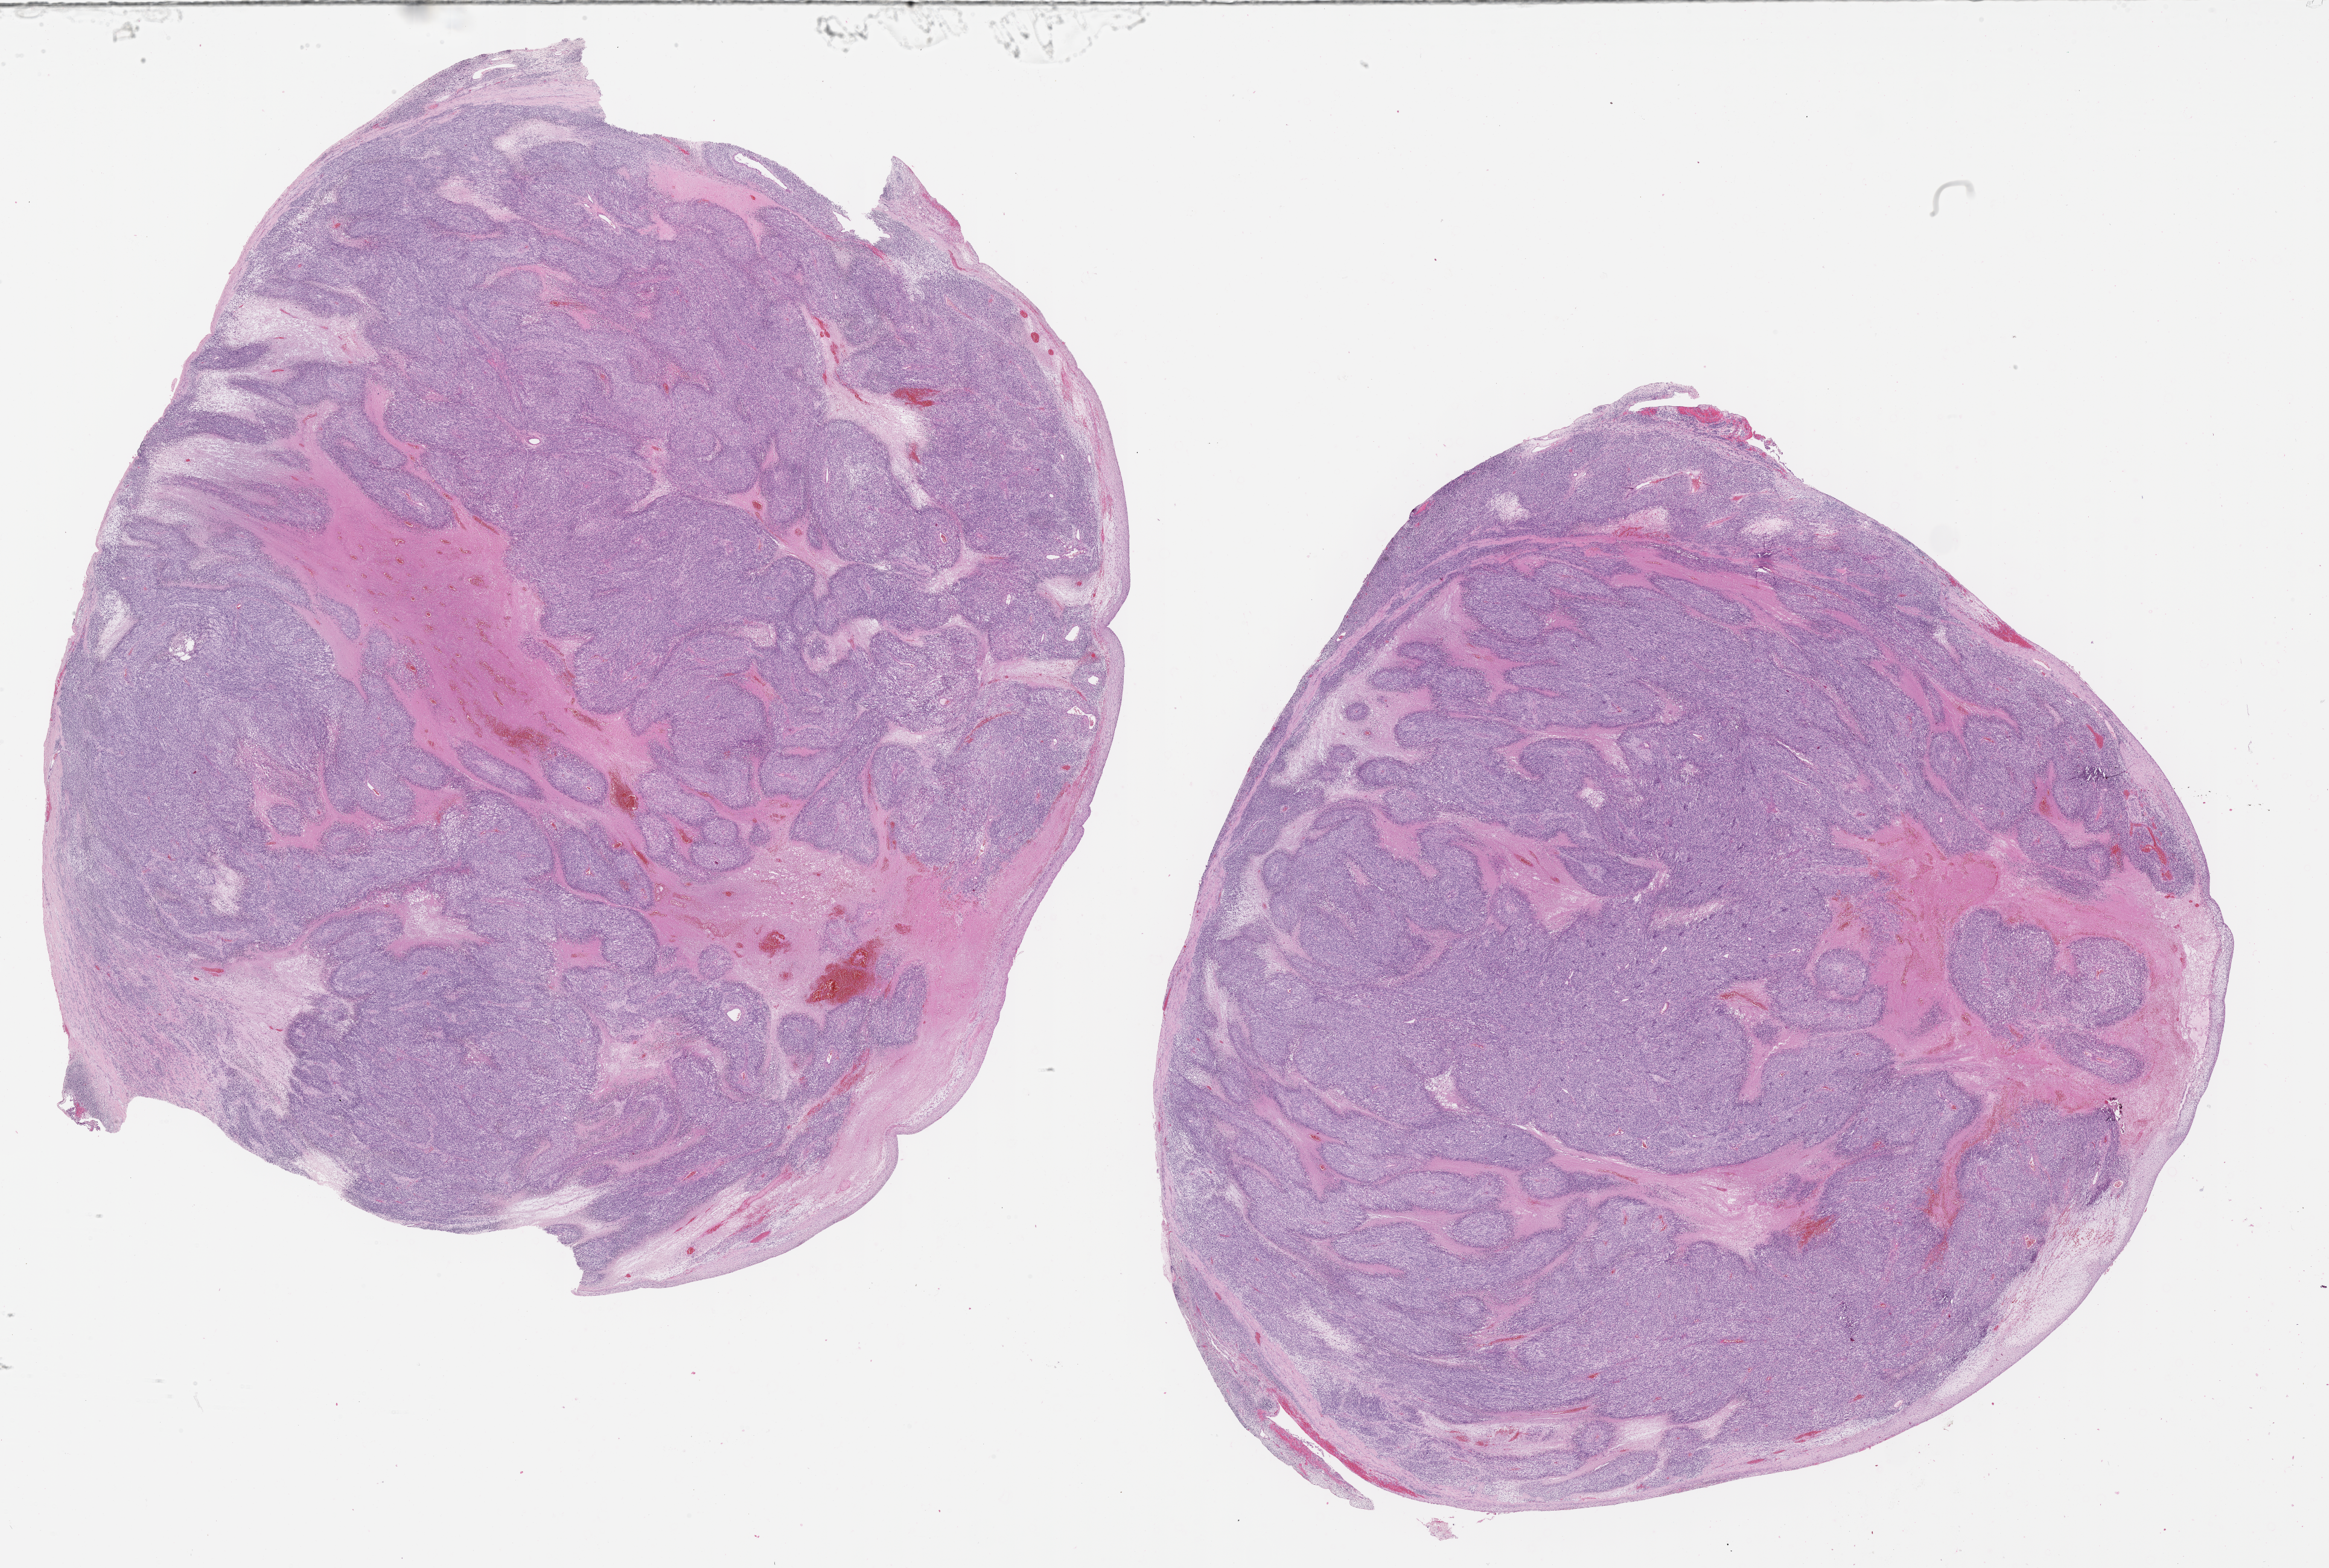
Digitized hematoxylin and eosin (H&E)-stained section of tumor tissue, a low-resolution overview of the entire scanned area, about 31.2 x 21.0 mm; formalin-fixed paraffin-embedded section; sample anatomic site: soft tissue - testicle, right. Male patient, age at diagnosis 8.2 years.
Primary site (case record): testis-Paratestis. Diagnosis: rhabdomyosarcoma; histological classification: embryonal rhabdomyosarcoma. Metastatic status at presentation (as recorded): non-metastatic. Stage (as recorded): 1.